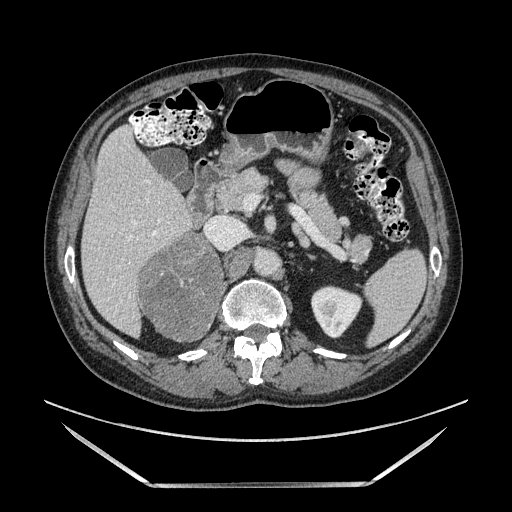
Contrast-enhanced abdominal CT, one axial slice. Slice 77 of 185 in the series (ordered by position). Soft-tissue window (W 400 / L 40 HU). 1.25 mm slice thickness. 512 × 512 image matrix, field of view 440 × 440 mm. Male patient. Case-level facts recorded for this patient, not image findings: diagnosis: adrenocortical carcinoma; tumour side: right adrenal; tumour size at pathology: 10.3 cm; Ki-67 index: 20 %; stage (as recorded): 3.
Annotated regions visible in this slice (semi-automatically segmented with operator editing):
- mass: box from (x=142, y=236) to (x=220, y=338) px